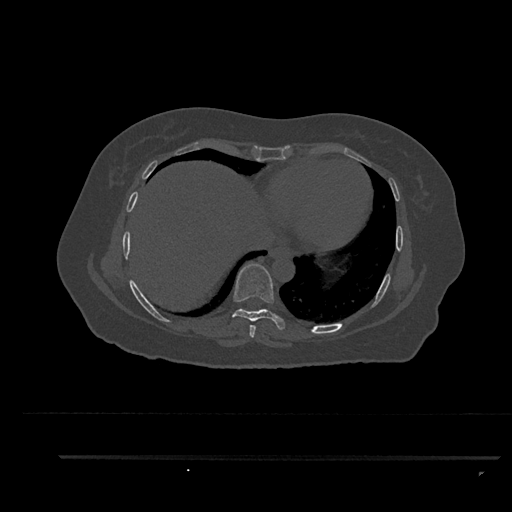
CT including the spine, one axial slice; position 460 of 797 along the scan axis; reconstruction kernel Br40s/3; 120 kVp; bone window (W 1800 / L 400 HU); 512 × 512 image matrix, field of view 408 × 408 mm. Female patient, age 44 years. From the clinical record (not read from this slice): primary cancer: renal; vertebrae with lytic lesions (as recorded): L1.
Annotated regions visible in this slice (semi-automatic segmentation, software-assisted and operator-edited):
- T7 vertebra: box from (x=249, y=325) to (x=256, y=338) px
- T8 vertebra: (x=232, y=263)–(x=286, y=330)